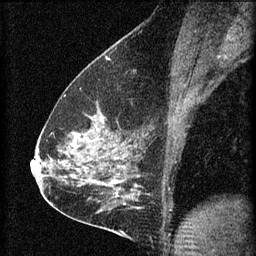
Breast MRI (dynamic contrast-enhanced), one sagittal slice; slice 38 of 60 in the series (ordered by position); 3 images stored at this slice position (order not interpretable as contrast timing); 1.5 T; TE 4.2 ms, TR 8.2 ms; 256 × 256 image matrix, field of view 180 × 180 mm. Female patient, age 59 years.
Annotated regions visible in this slice (semi-automatic segmentation, software-assisted and operator-edited):
- analysis volume of interest (the breast-tissue region the enhancement analysis was run in; not a lesion): bounding box (x1, y1, x2, y2) in pixels: (61, 104, 134, 161)
- tumour enhancement mask (voxels above the 70 % enhancement threshold inside the analysis volume of interest): (72, 118, 99, 149)